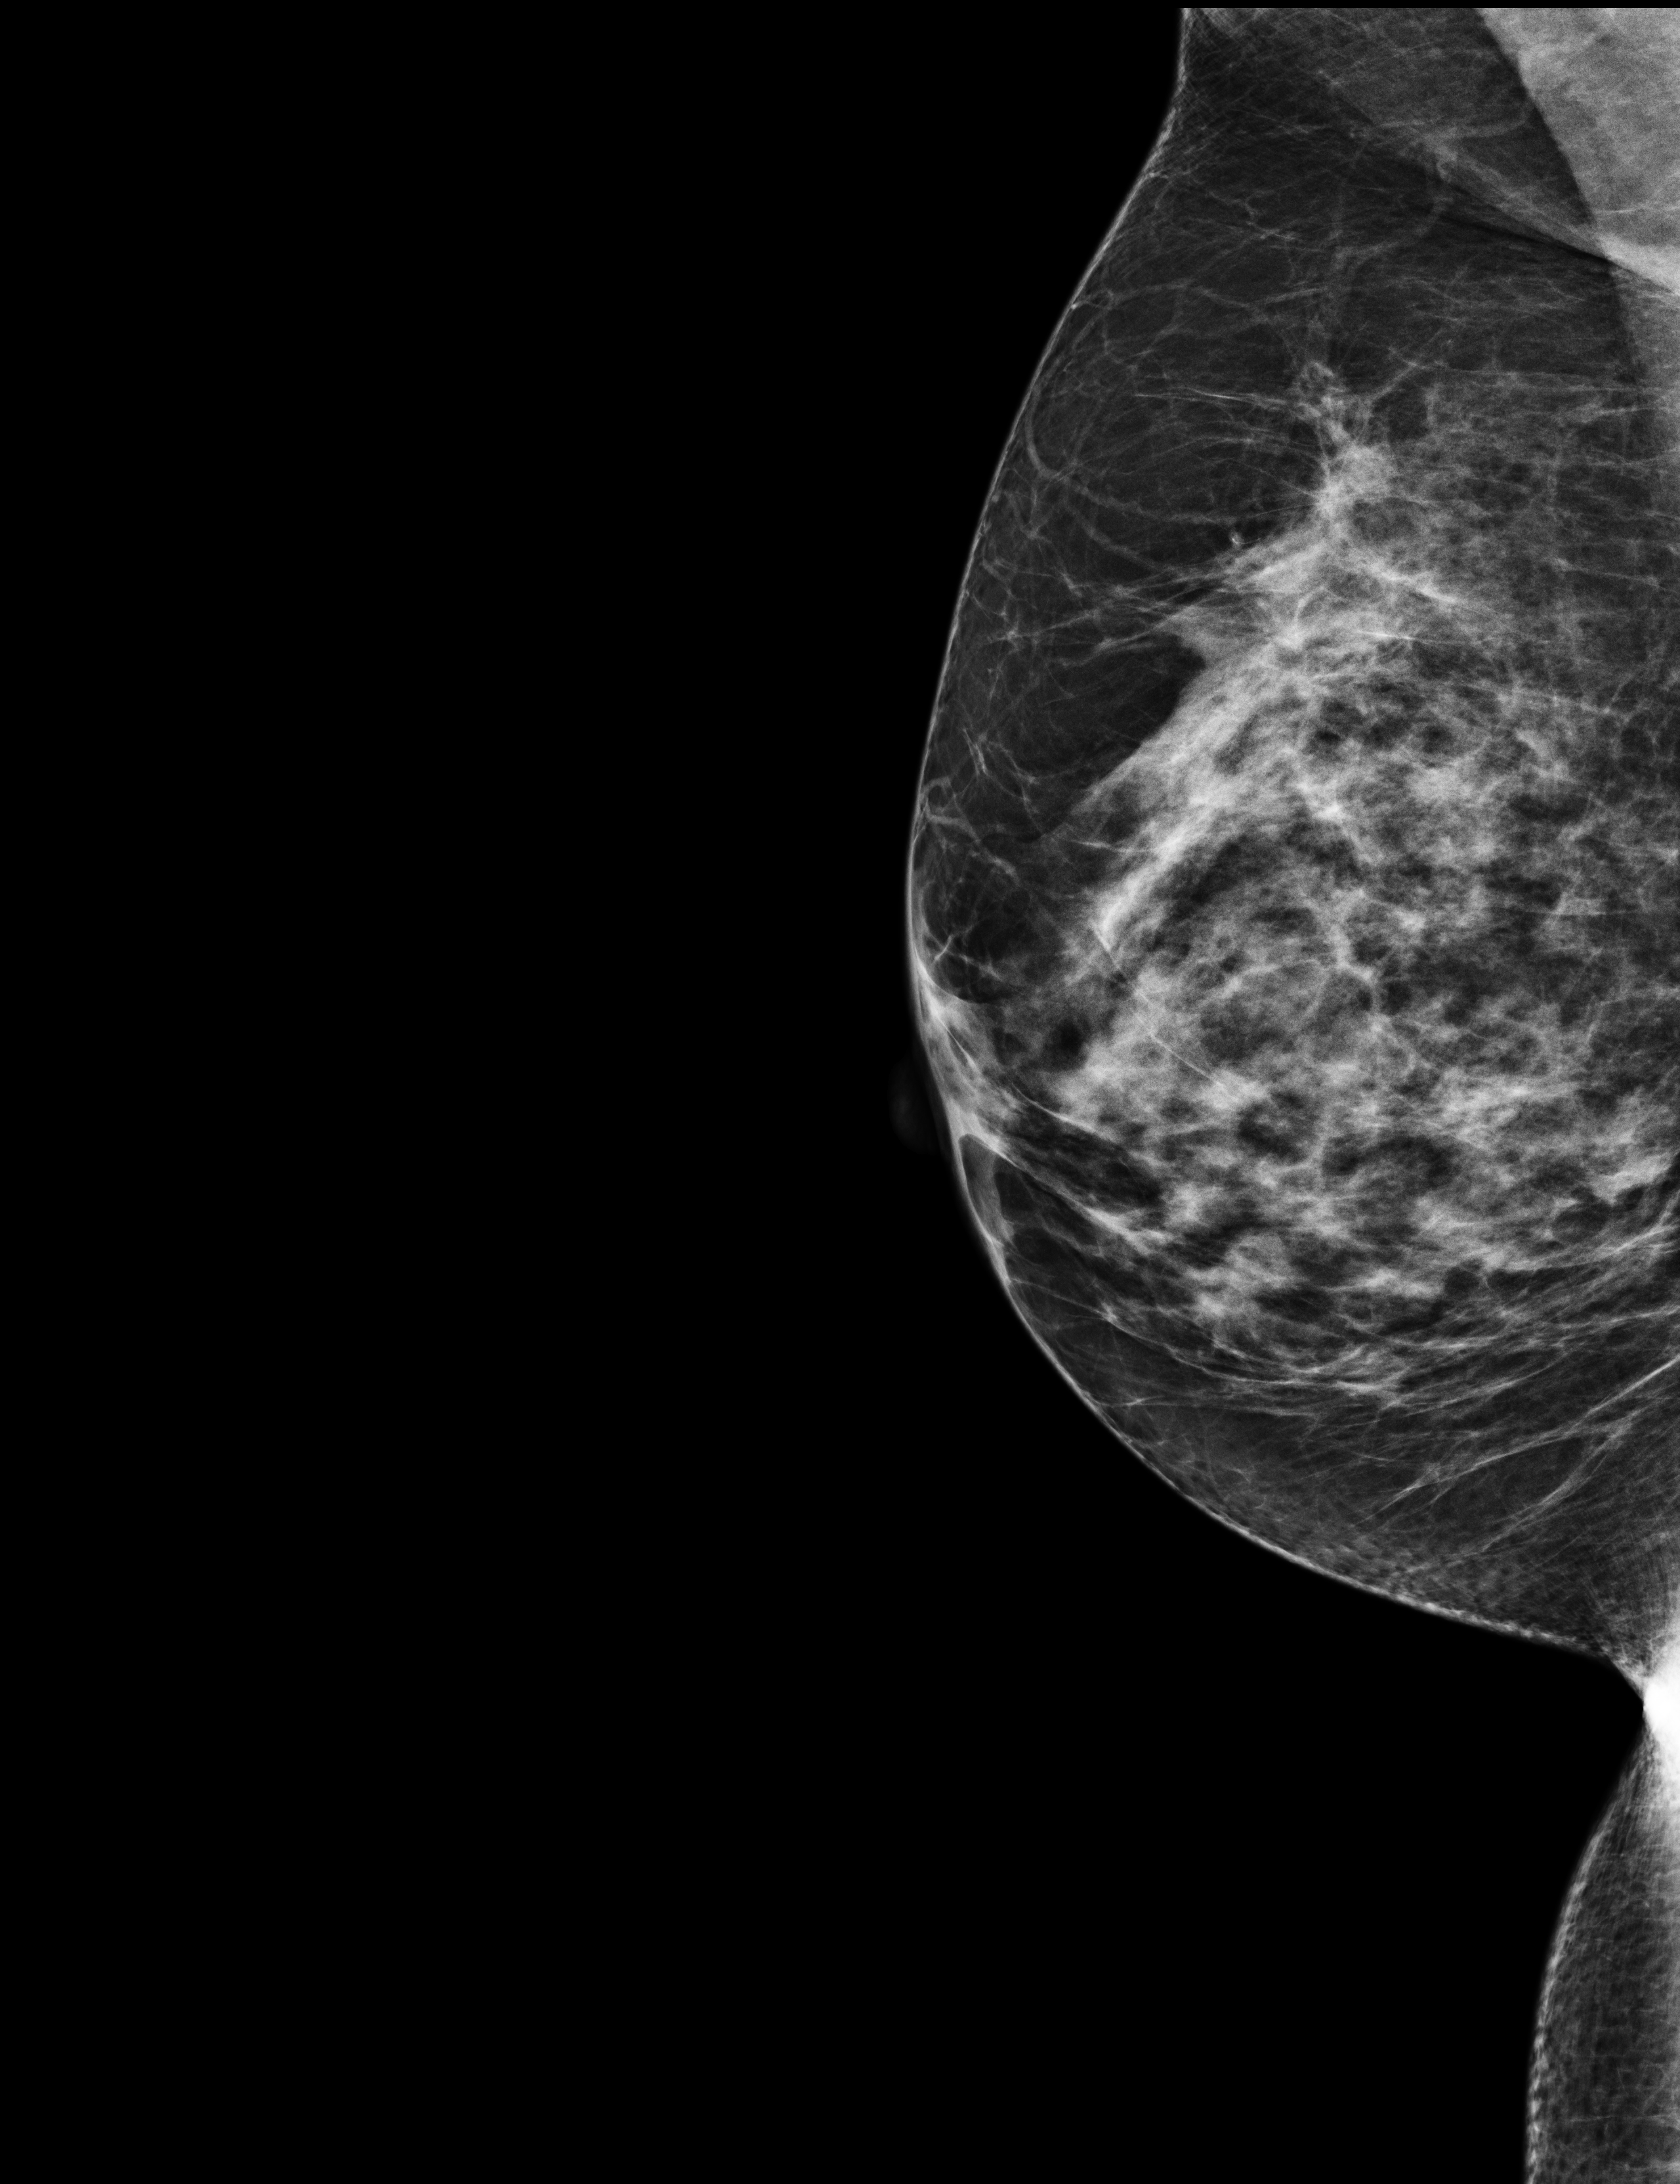
Annual screening mammography examination; compressed breast thickness 56 mm; system: Selenia Dimensions. Patient: female, 59 years.
Image type: full-field digital mammogram. Breast: right. Projection: MLO view.